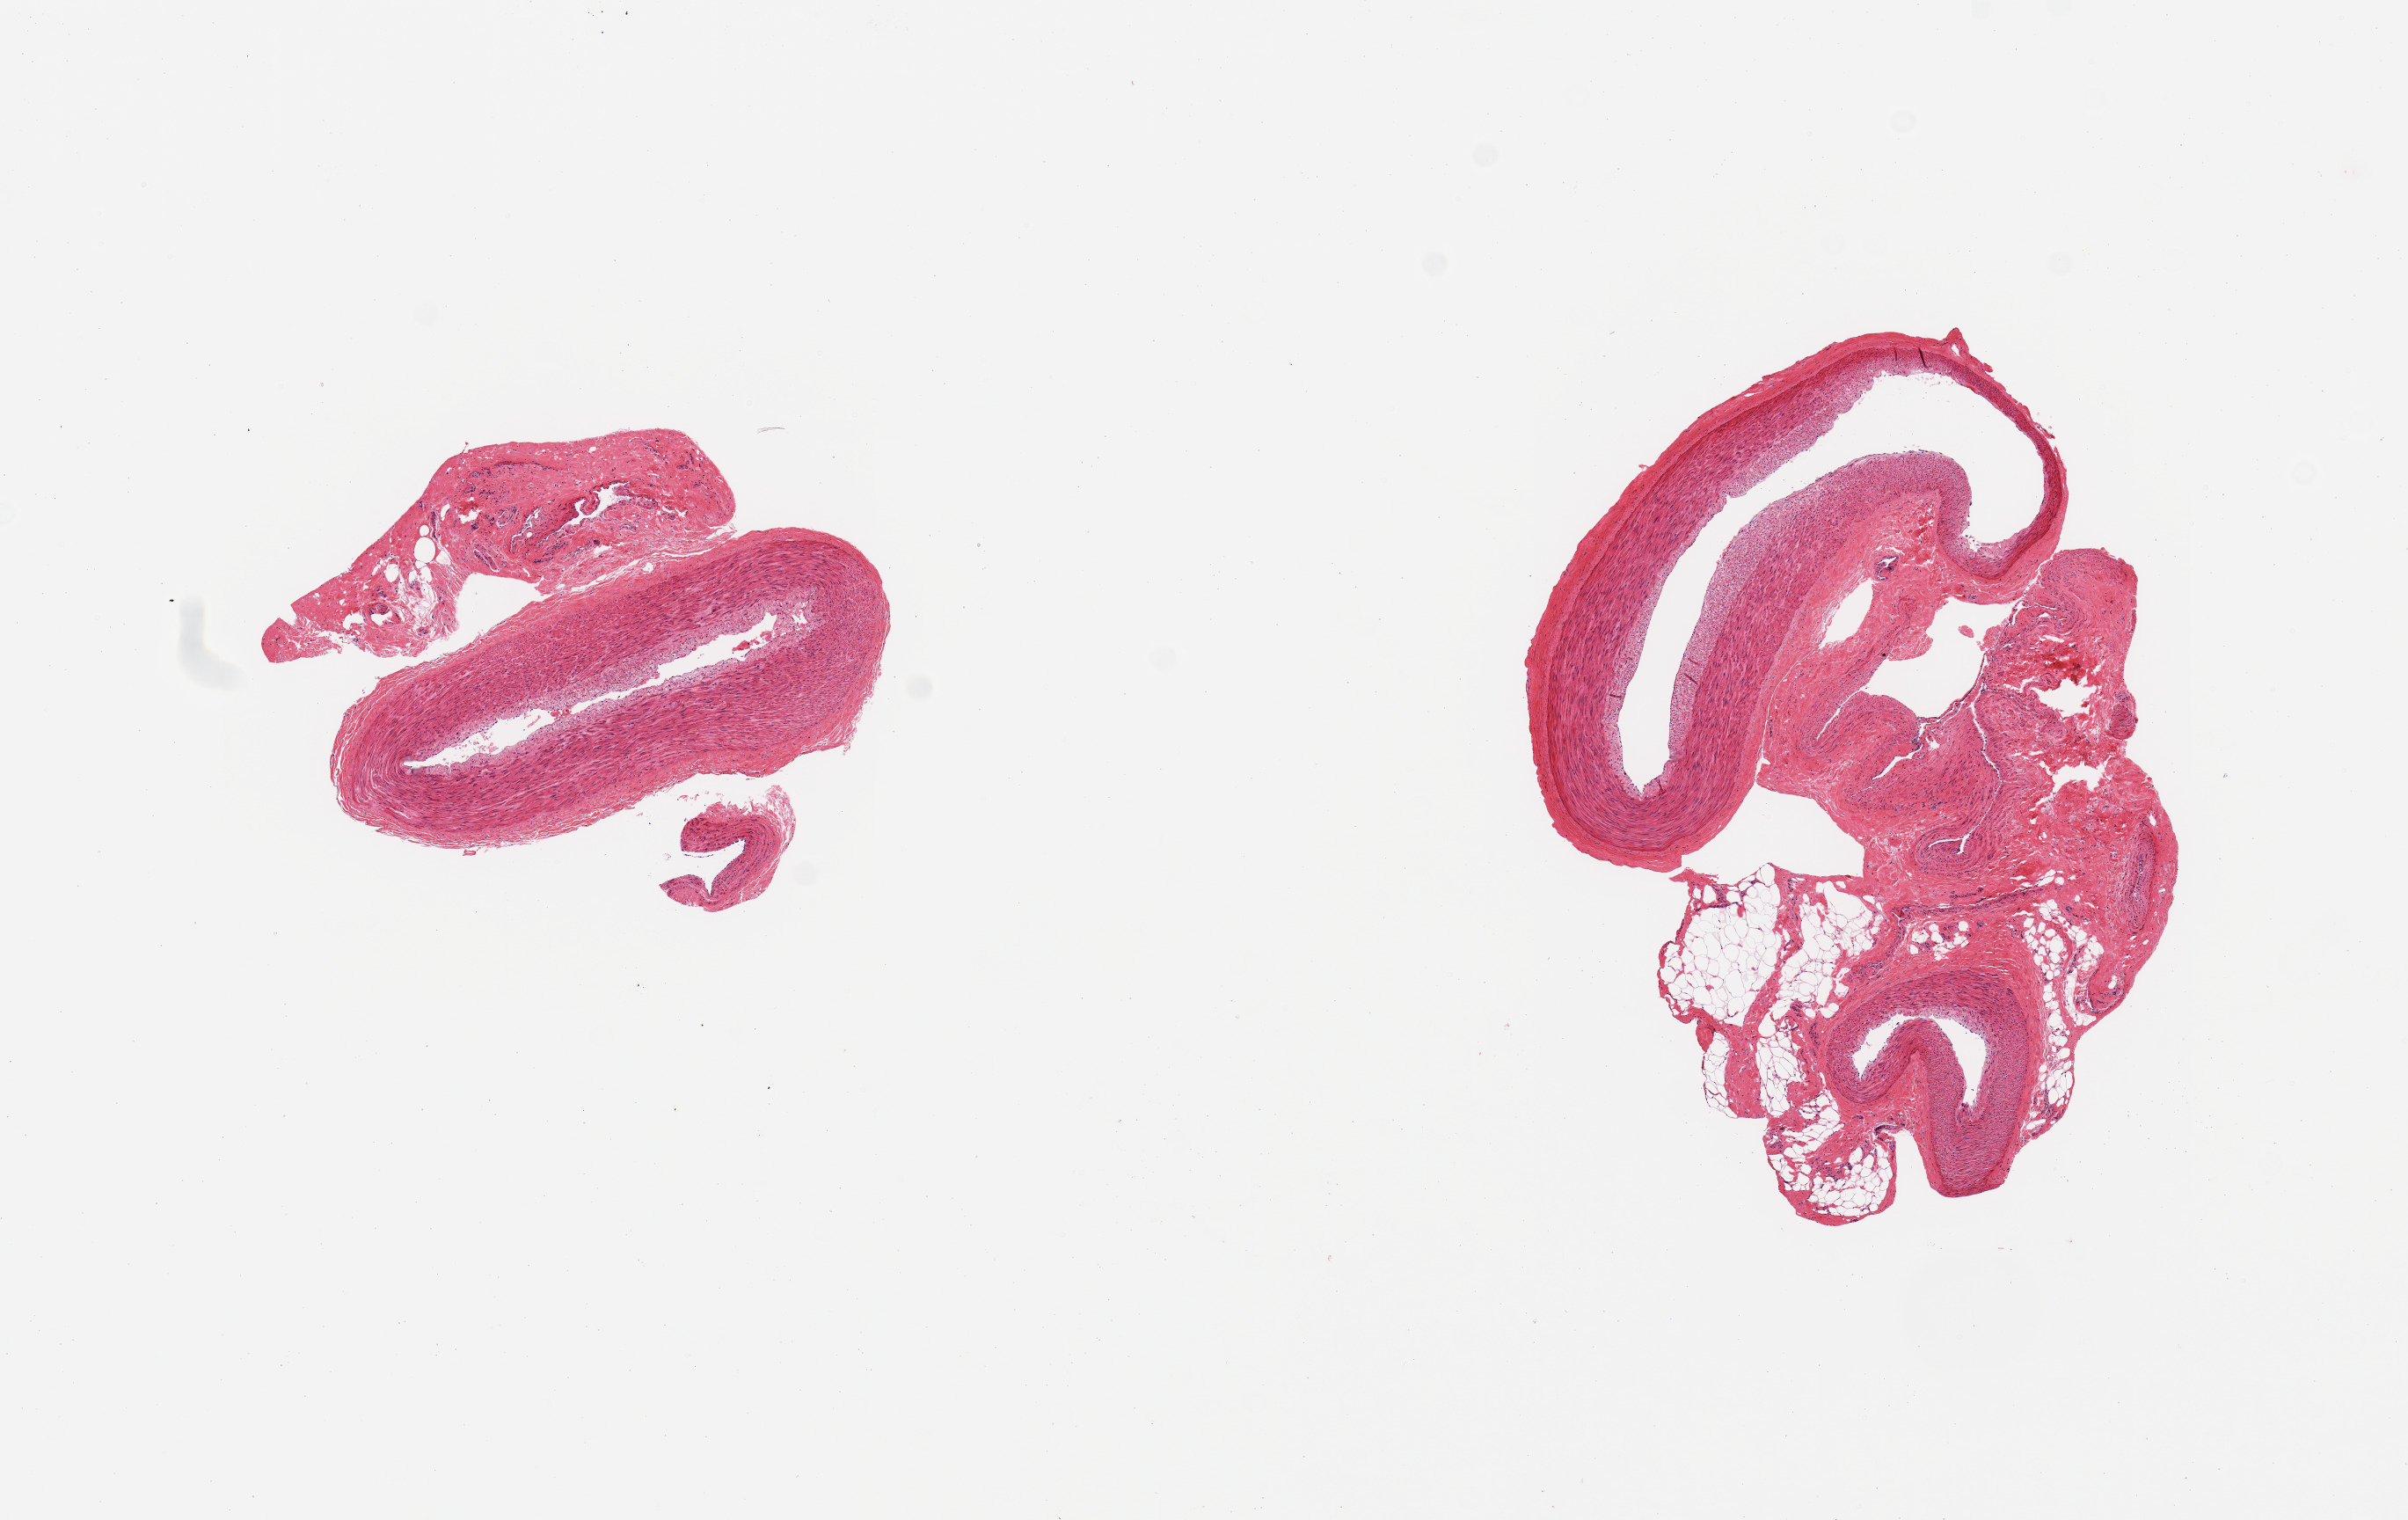
Whole-slide image, haematoxylin and eosin stain, brightfield — low-resolution overview of the scanned area, about 10.8 x 6.8 mm (from a 20x scan). PAXgene-fixed, paraffin-embedded tissue. Target tissue: tibial artery. Tissue donor sample.
* pathologist's review note for this sample: 2 pieces; includes attachment of fat/fibrous tissue/vessels from 30-60%